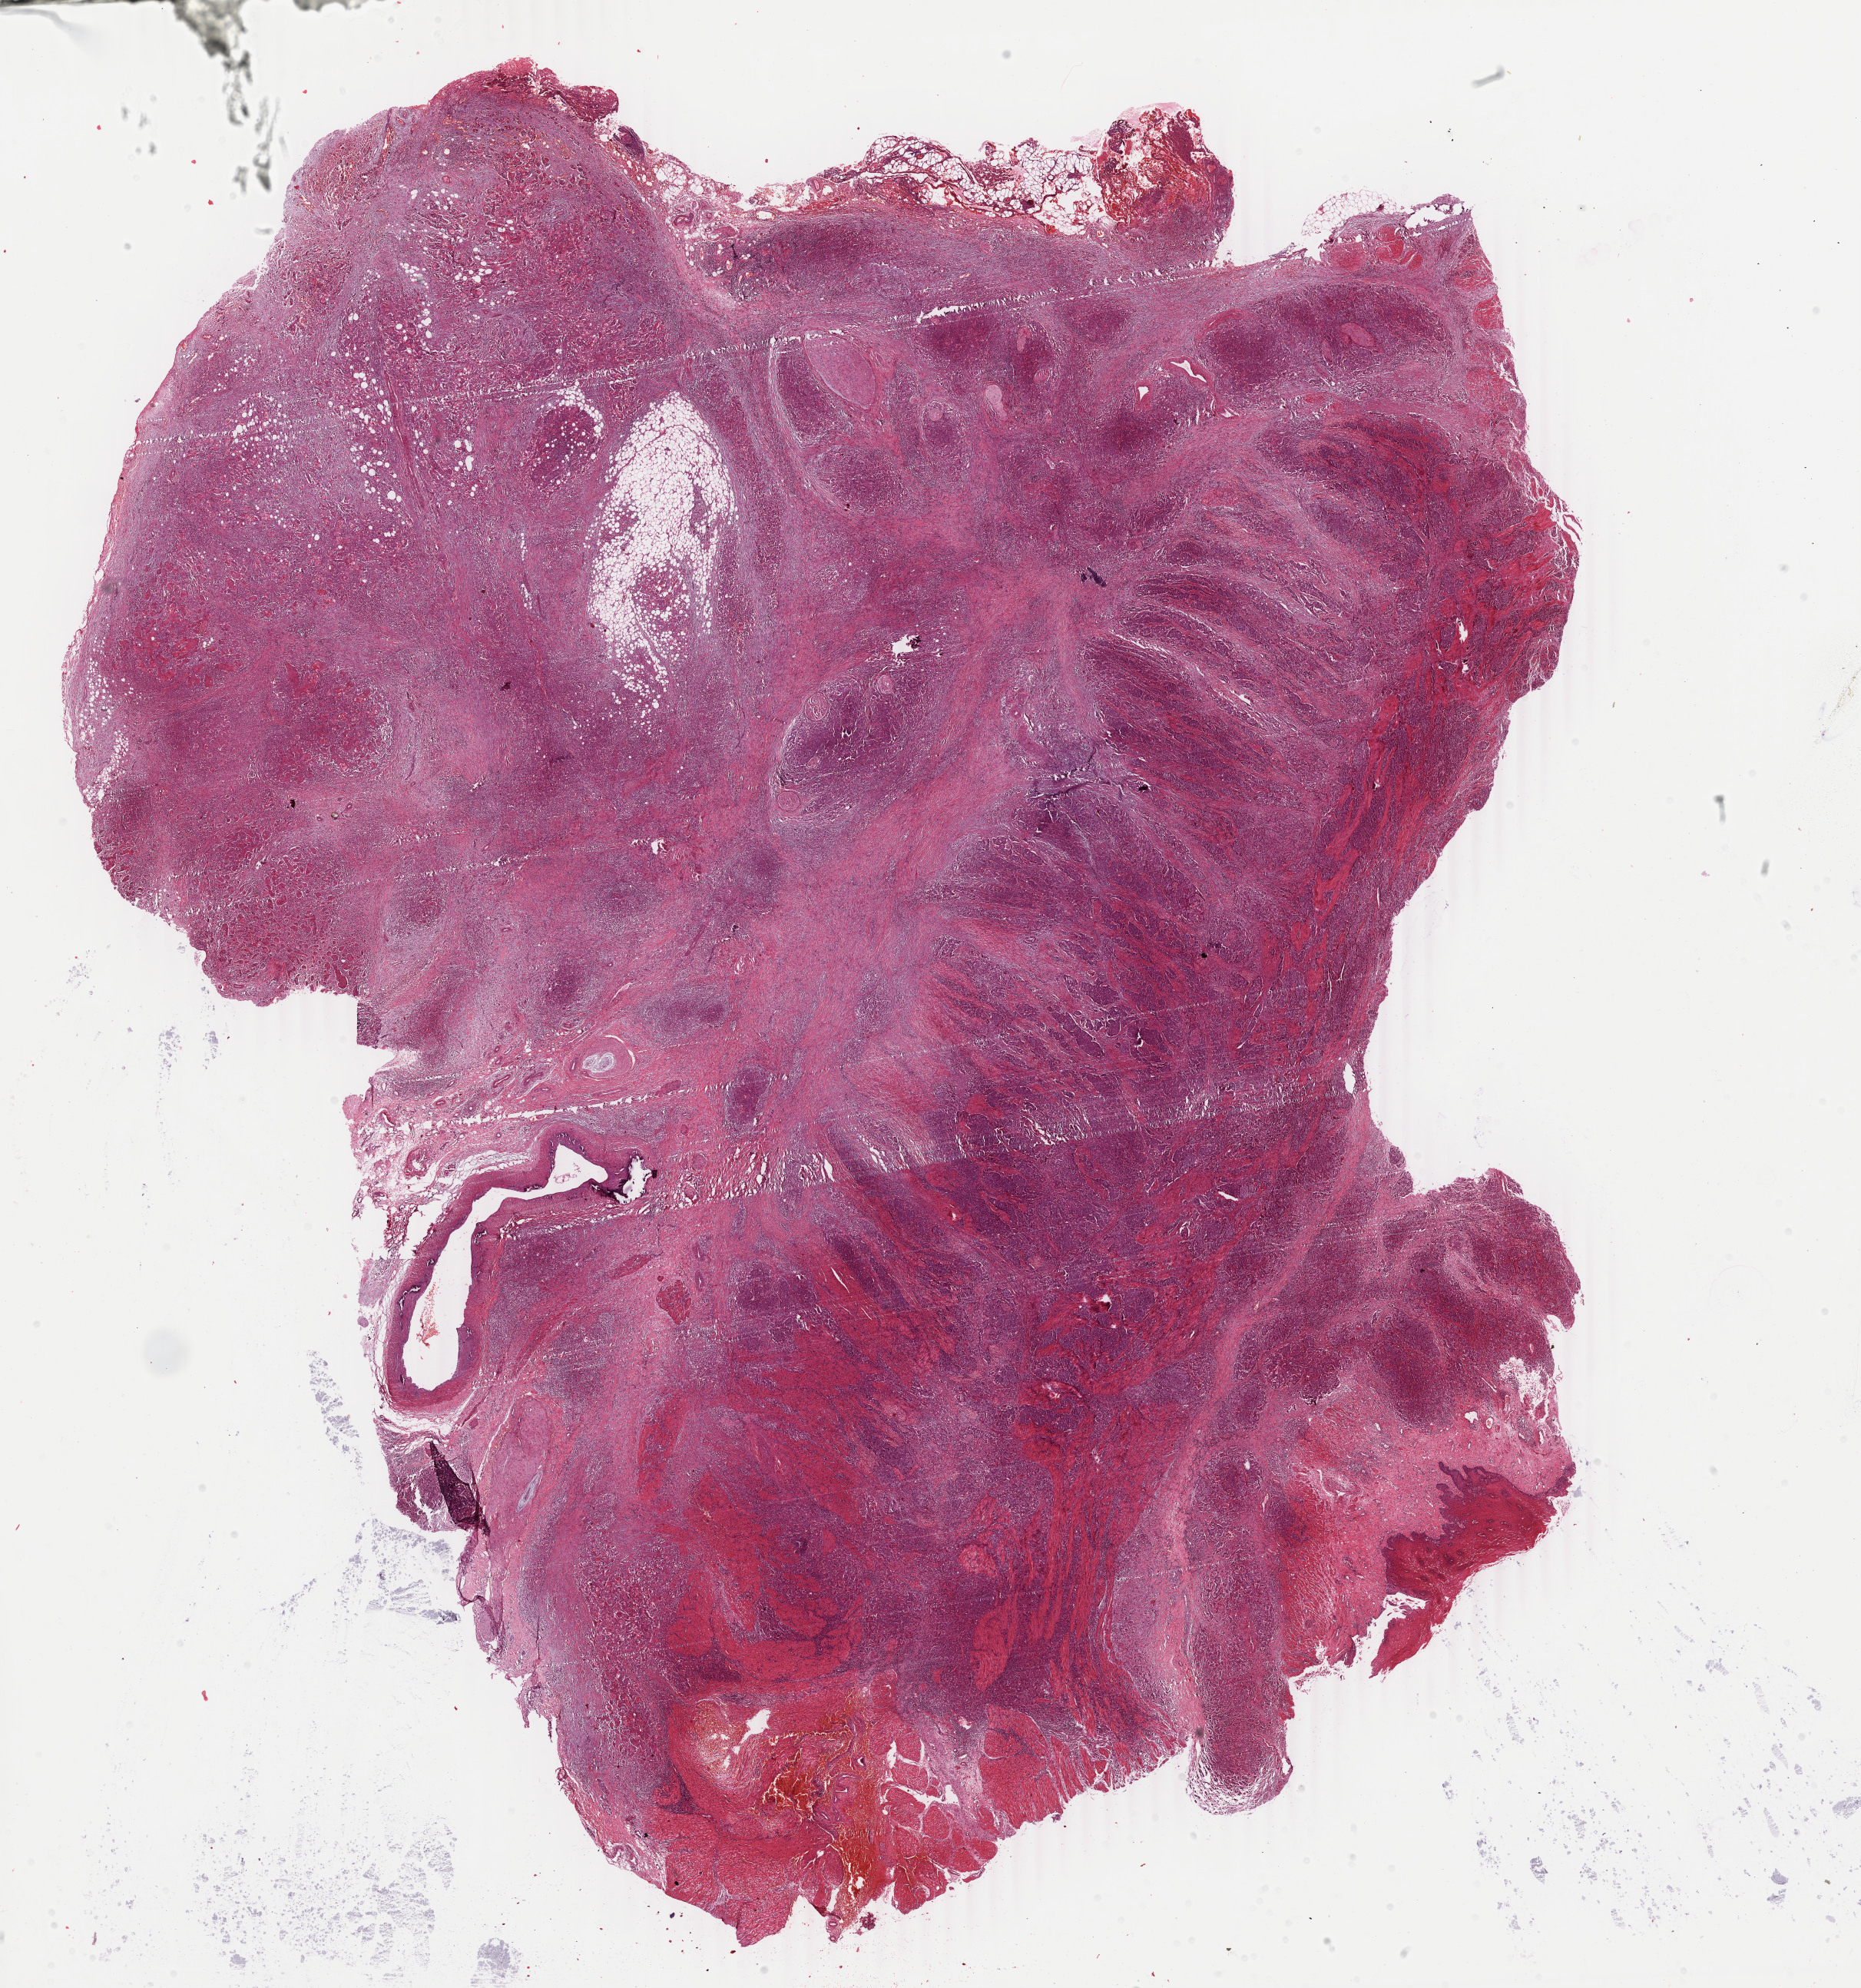
H&E-stained whole-slide image, low-resolution overview of the scanned area, about 19.3 x 20.6 mm (from a 40x scan). FFPE section. Primary tumour sample from the esophagus. Patient: male, age at initial diagnosis 71 years. Histologic grade: G2 (moderately differentiated).
- diagnosis: Squamous cell carcinoma, NOS (lower third of esophagus)
- AJCC pathologic stage: IIA